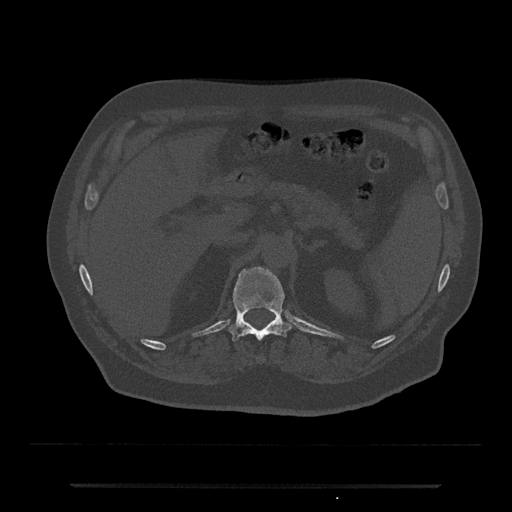
CT including the spine, one axial slice; slice 594 of 797 in the series (ordered by position); reconstruction kernel Br40s/3; bone window (W 1800 / L 400 HU); 0.5 mm slice thickness; 512 × 512 image matrix. Male patient, age 80 years. Case-level facts recorded for this patient, not image findings: primary cancer: prostate; vertebrae with lytic lesions (as recorded): L1, T11.
Annotated regions visible in this slice (semi-automatically segmented with operator editing):
- T12 vertebra: bounding box <228,267,291,342> (left, top, right, bottom; pixels)